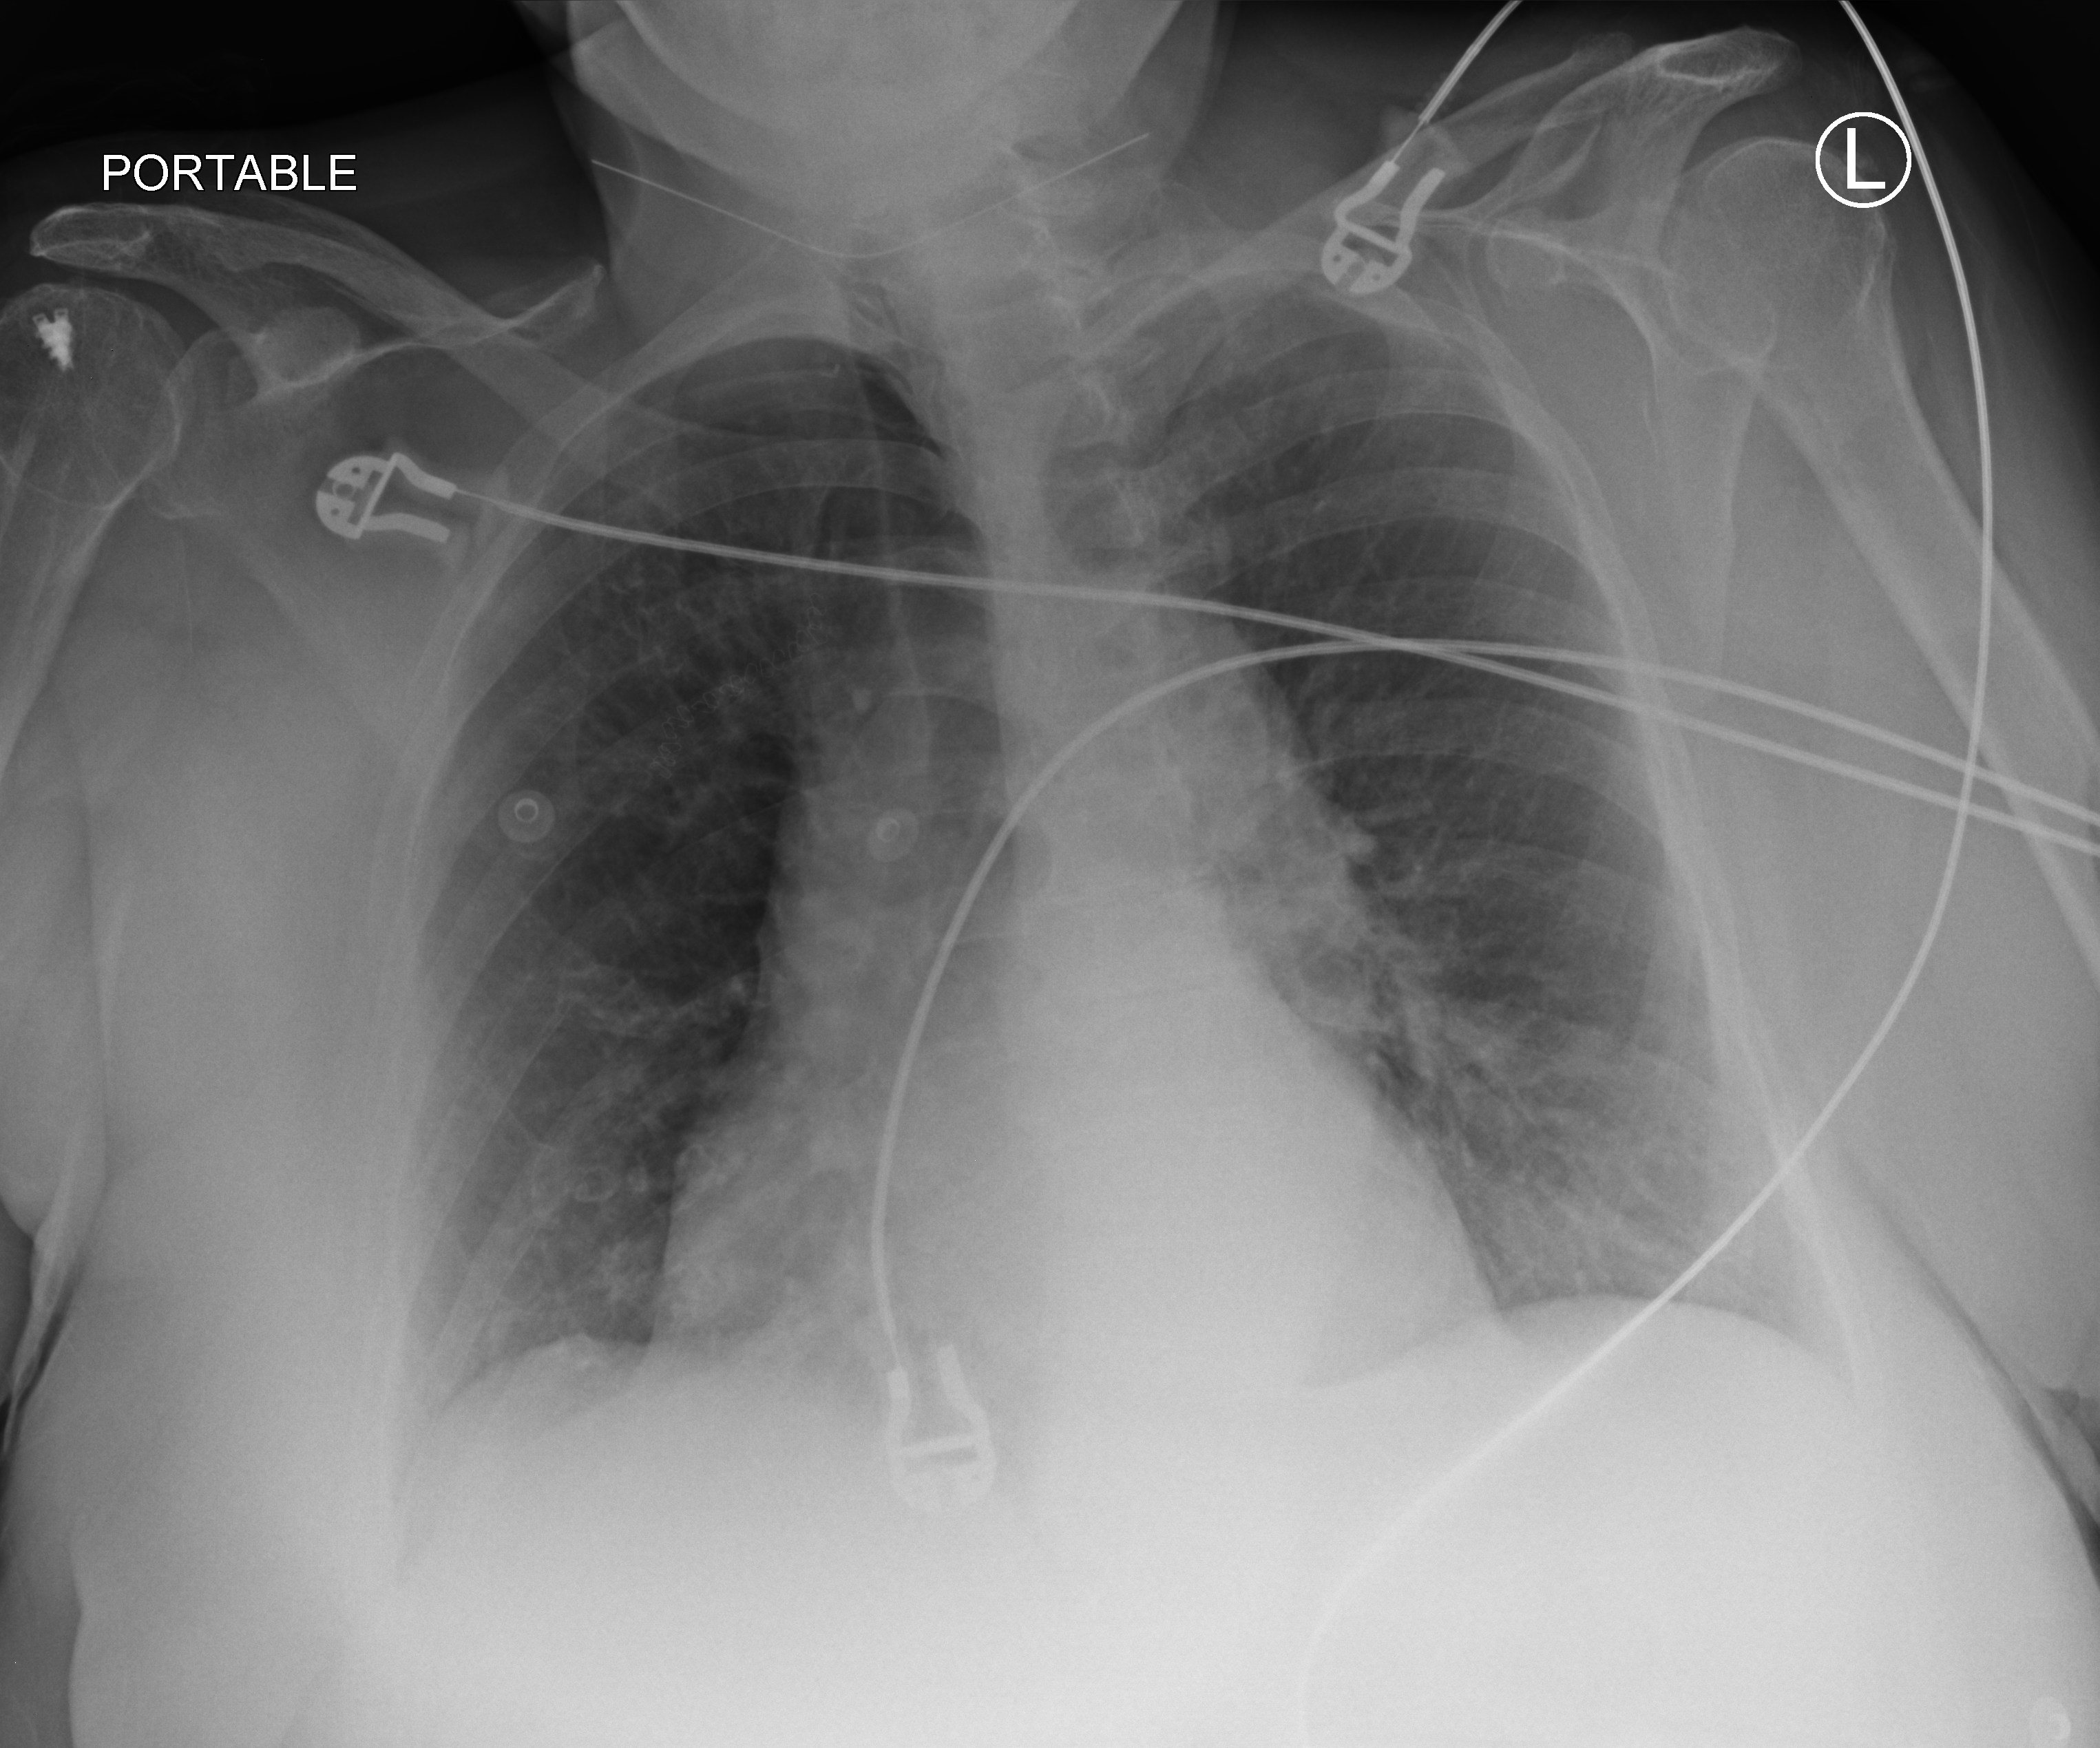
Bedside chest radiograph (computed radiography), anteroposterior (AP) projection. Patient hospitalised with COVID-19; female, aged 75–90 years.
From the hospital-stay record, not from the radiograph (when in the stay this image was taken is not recorded): hypertension (admission record): yes.